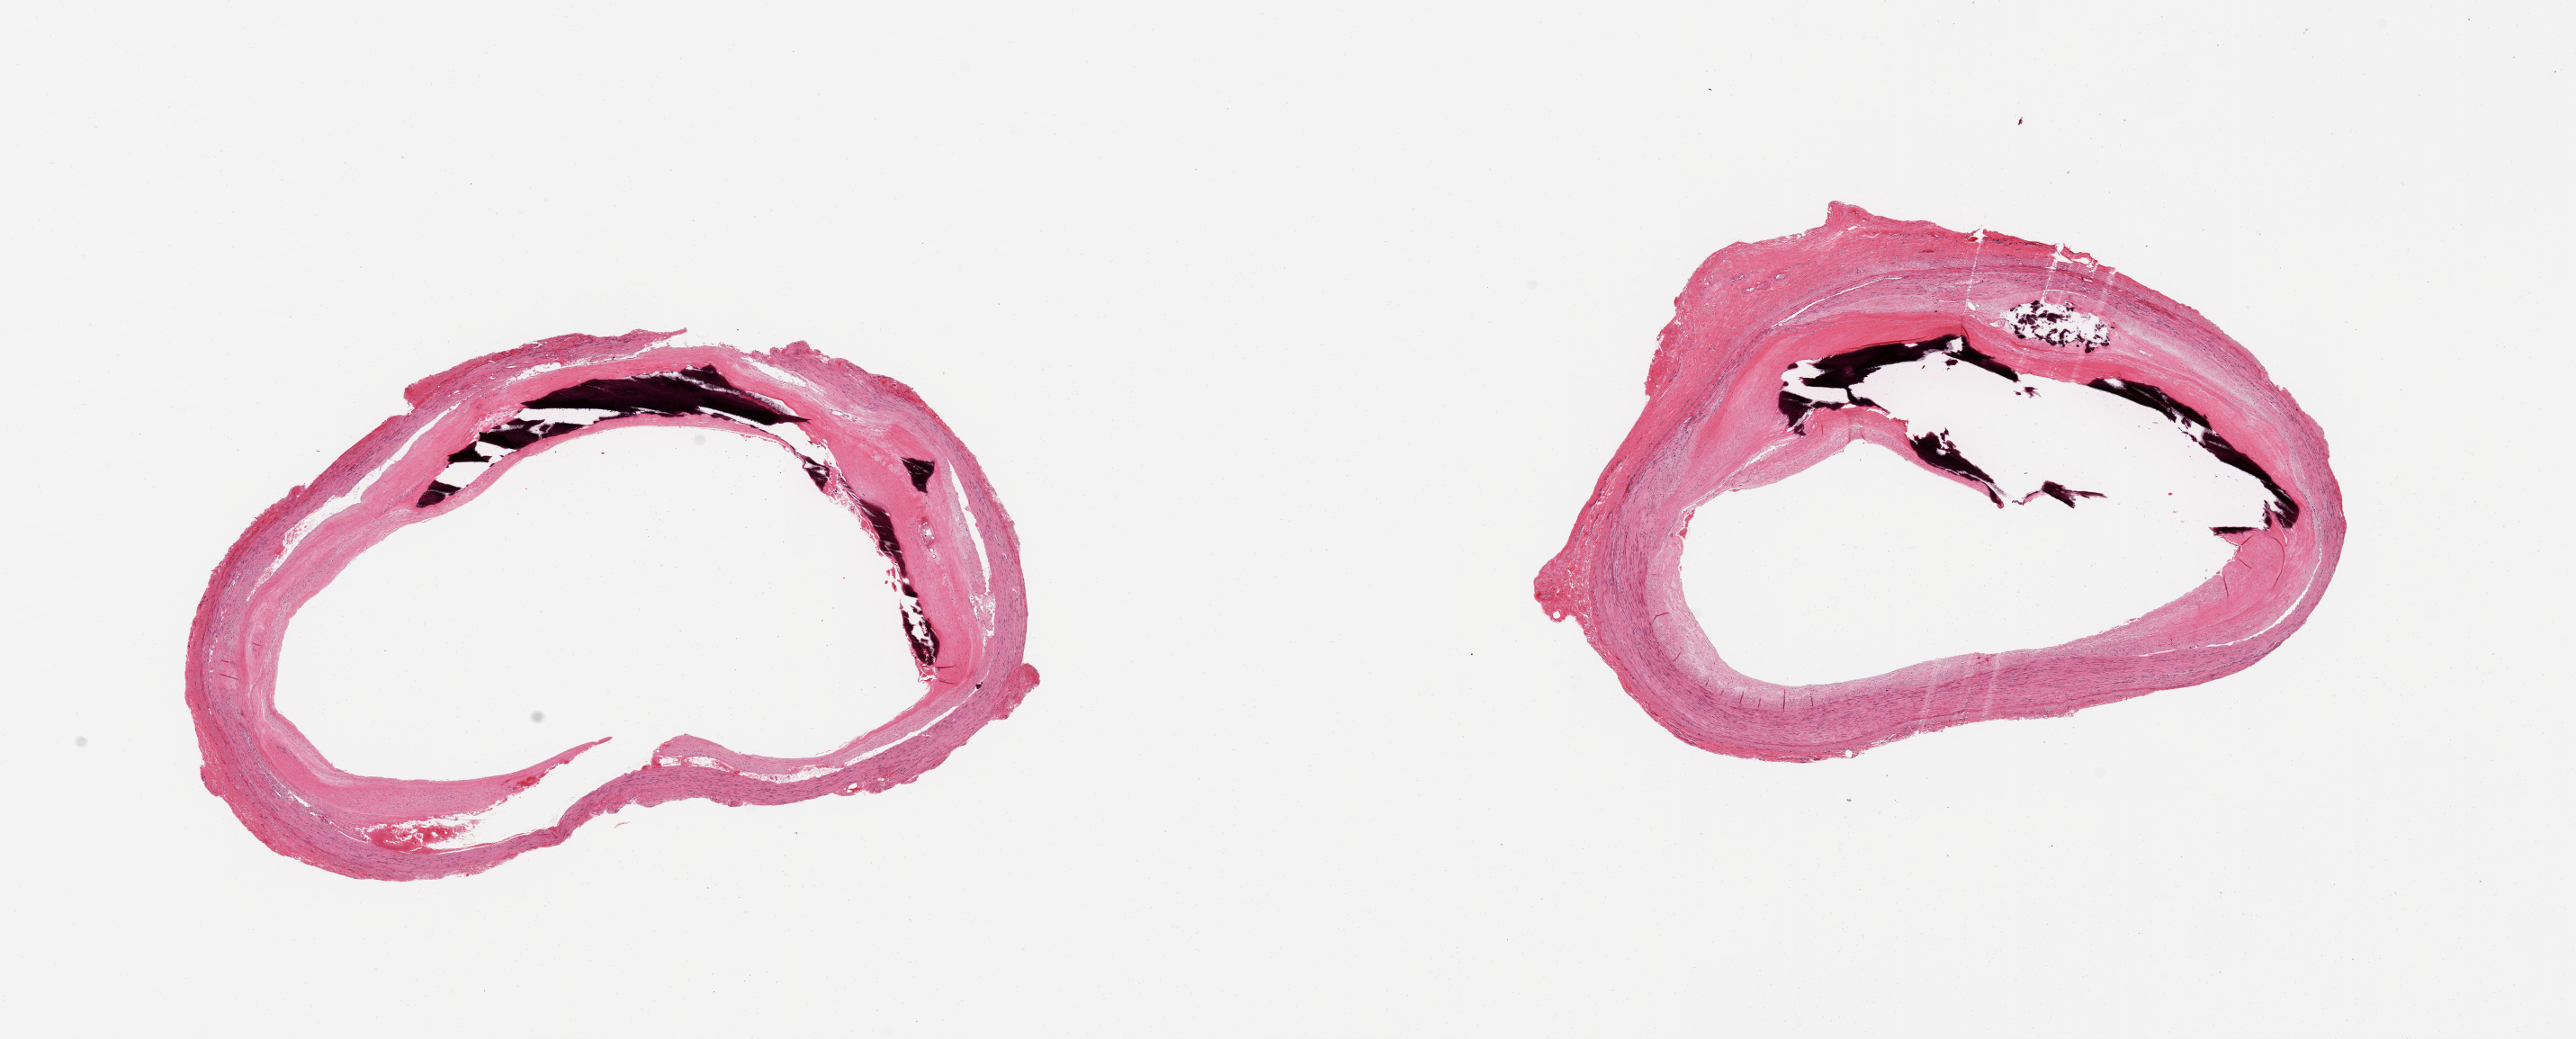
Whole-slide image, H&E stain — low-resolution overview of the scanned area, about 22.6 x 9.1 mm, PAXgene-fixed, paraffin-embedded tissue, section of tibial artery (target tissue), tissue donor sample.
Reviewer comment on this tissue sample: 2 pieces; arteriosclerosis with intimal and medial calcifications.